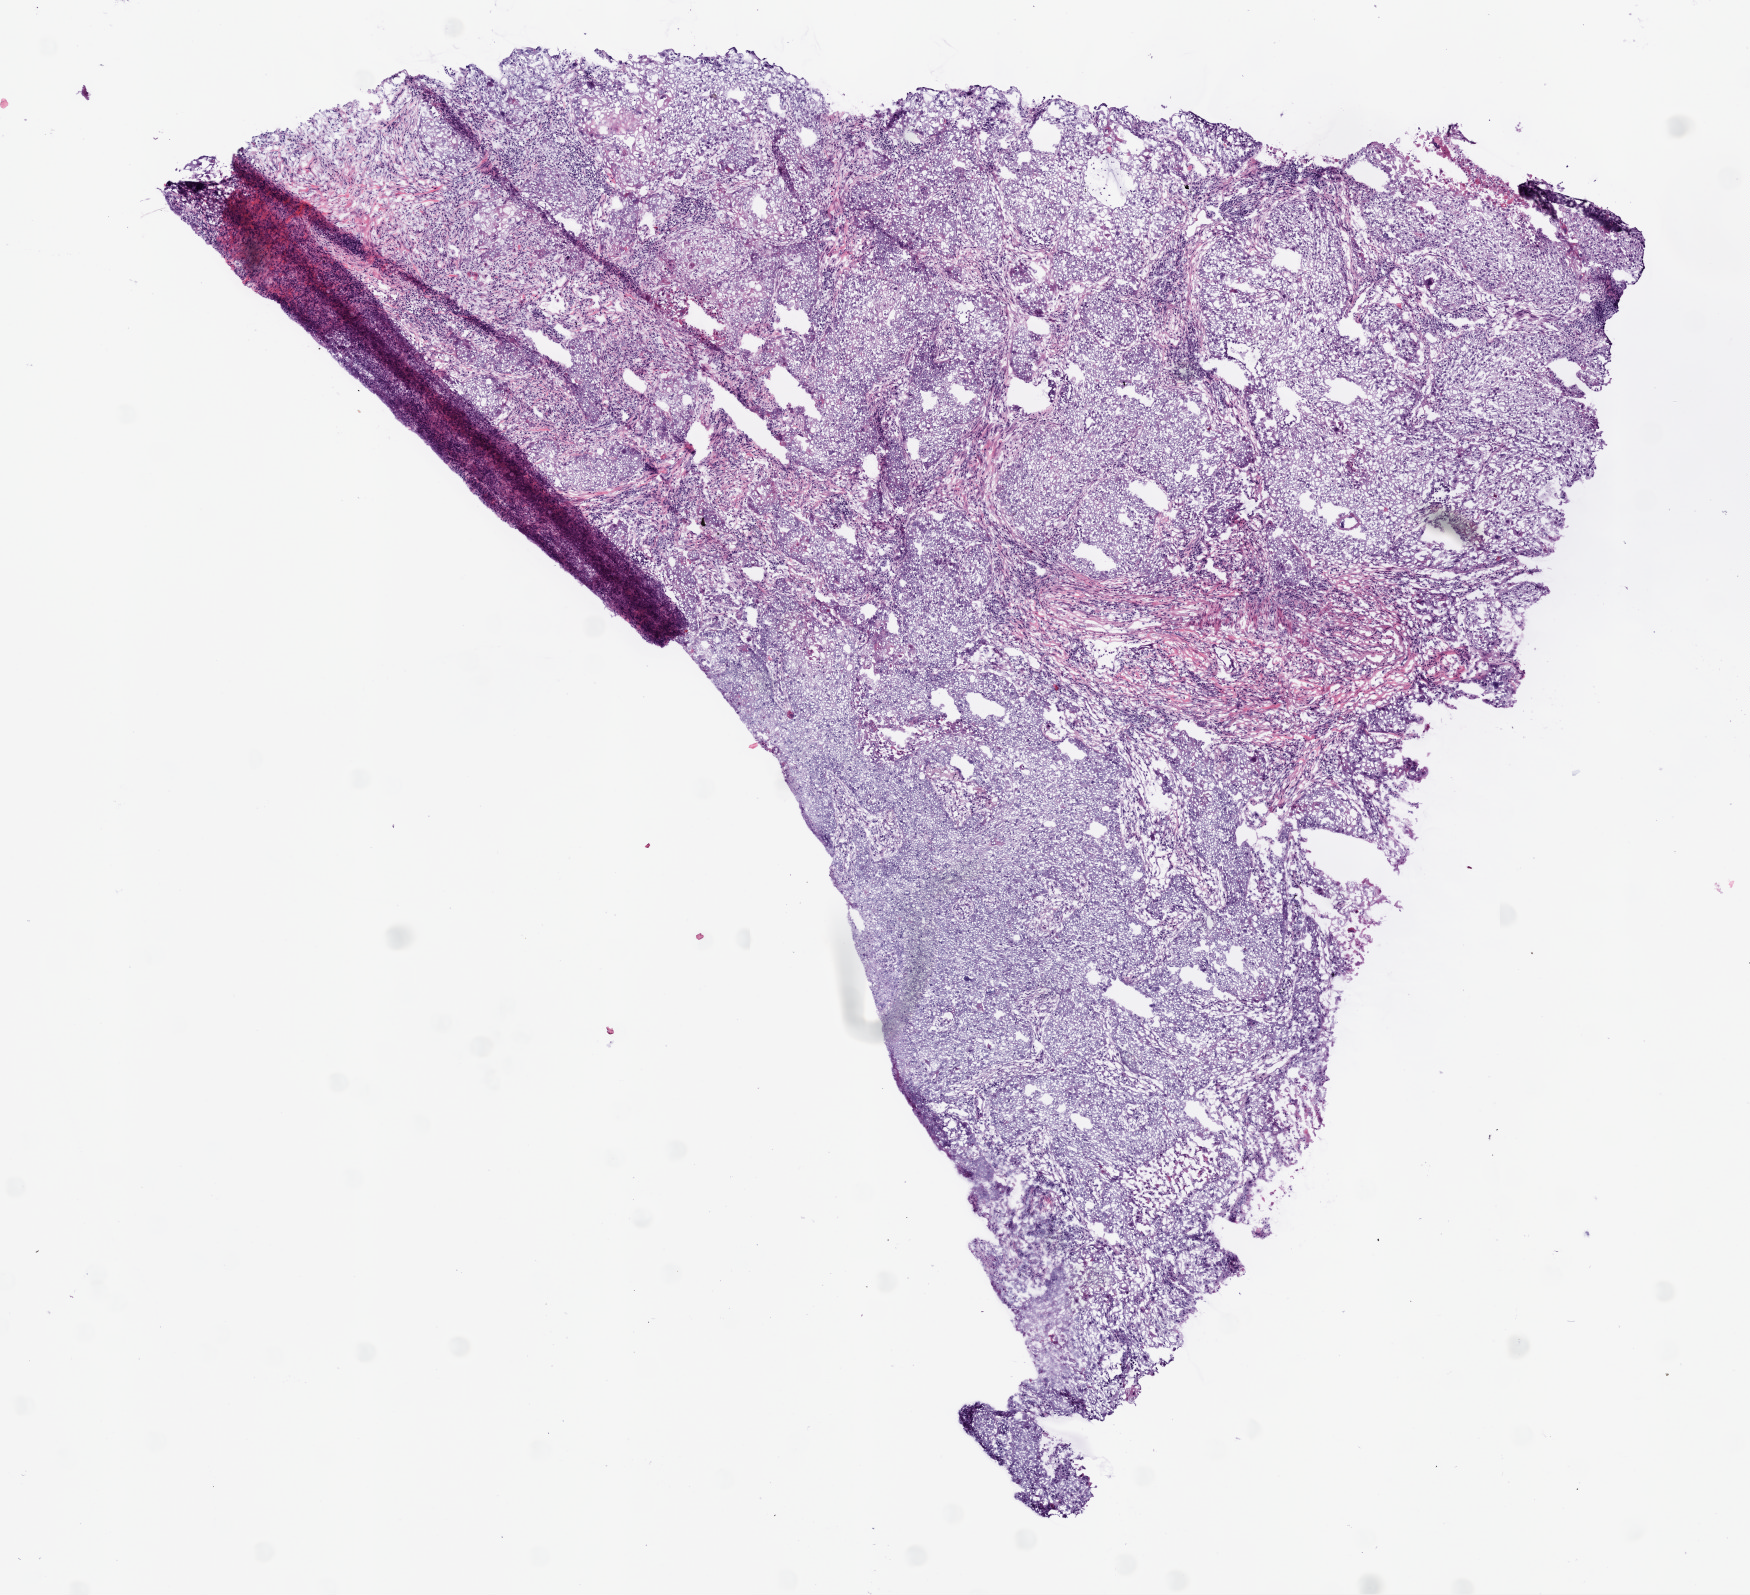
Digitized H&E-stained tissue section (whole slide), whole scanned area (about 7.0 x 6.4 mm) shown as a low-resolution overview, frozen section from the bottom of the tissue portion, sample: primary tumour, lung. Male patient; age at initial diagnosis 77 years. Pathologist review of this section (percent, as recorded): tumour cells 80%, tumour nuclei 80%, normal cells 0%, stromal cells 15%, necrosis 5%. Infiltration values recorded for this section: lymphocyte infiltration 5%.
• pathologic diagnosis: Squamous cell carcinoma, NOS (upper lobe, lung)
• AJCC pathologic stage: IB